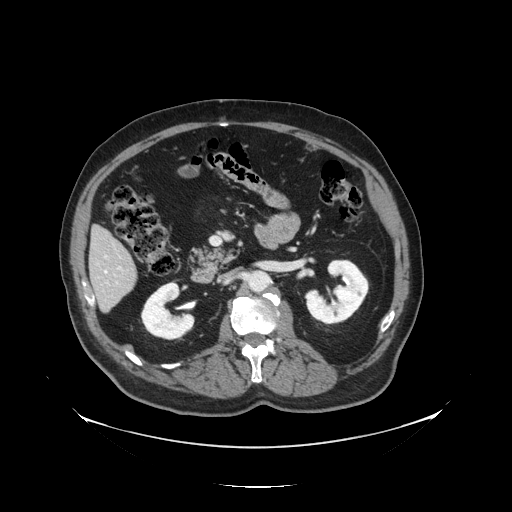
Contrast-enhanced abdominal CT, one axial slice; slice 53 of 138 in the series (ordered by position); reconstruction kernel STANDARD; 120 kVp; intravenous contrast given; soft-tissue window (W 400 / L 40 HU); 2.5 mm slice thickness; 512 × 512 image matrix. Male patient, age 77 years. Case-level facts recorded for this patient, not image findings: diagnosis: colorectal cancer liver metastases, imaged before liver resection; multiple liver metastases: no; largest metastasis: 1.5 cm.
Outlined on this slice (expert manual segmentation):
- liver: bounding box (x1, y1, x2, y2) in pixels: (91, 230, 138, 310)
- planned liver remnant (the part of the liver to remain after resection): (91, 230, 136, 281)